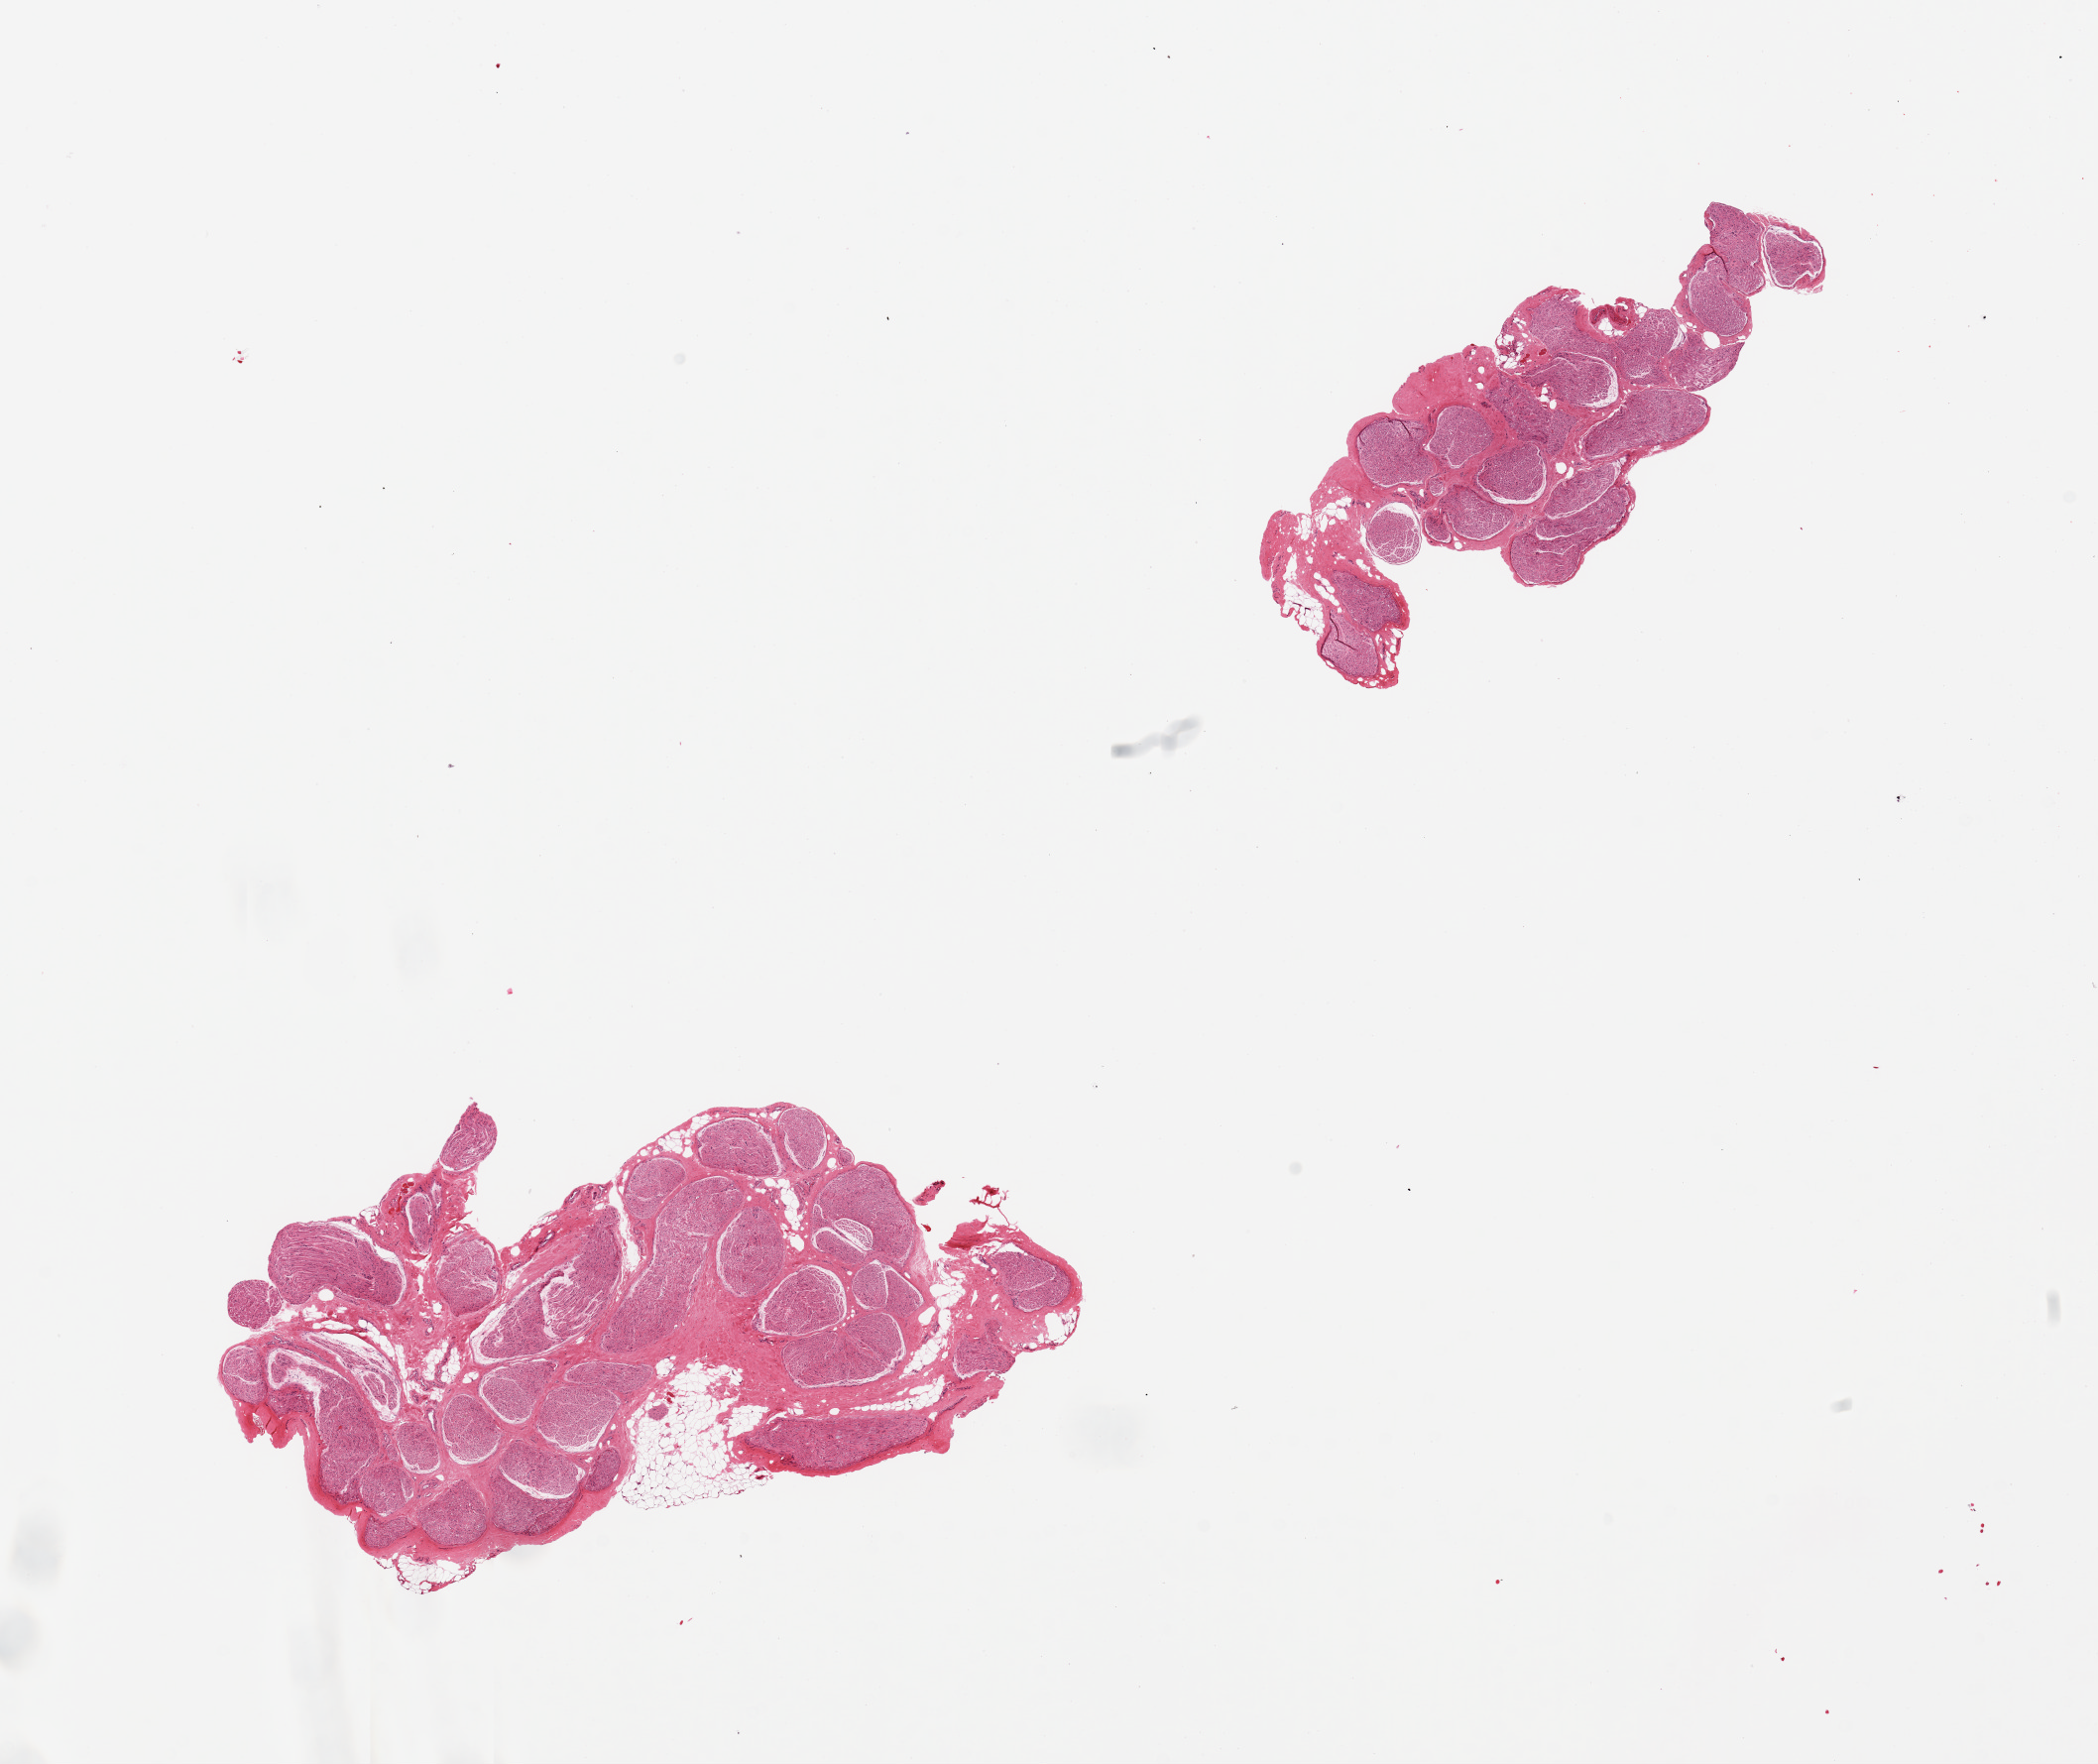
Whole-slide image, haematoxylin and eosin stain, whole scanned area (about 16.7 x 14.1 mm, slide scanned at 20x) shown as a low-resolution overview, PAXgene-fixed paraffin-embedded (PFPE) section, section of tibial nerve (target tissue), donor tissue sample. Donor sex: female.
- reviewer comment on this tissue sample: 2 pieces, good specimens, small ~1mm nubbin of fat on one aliquot